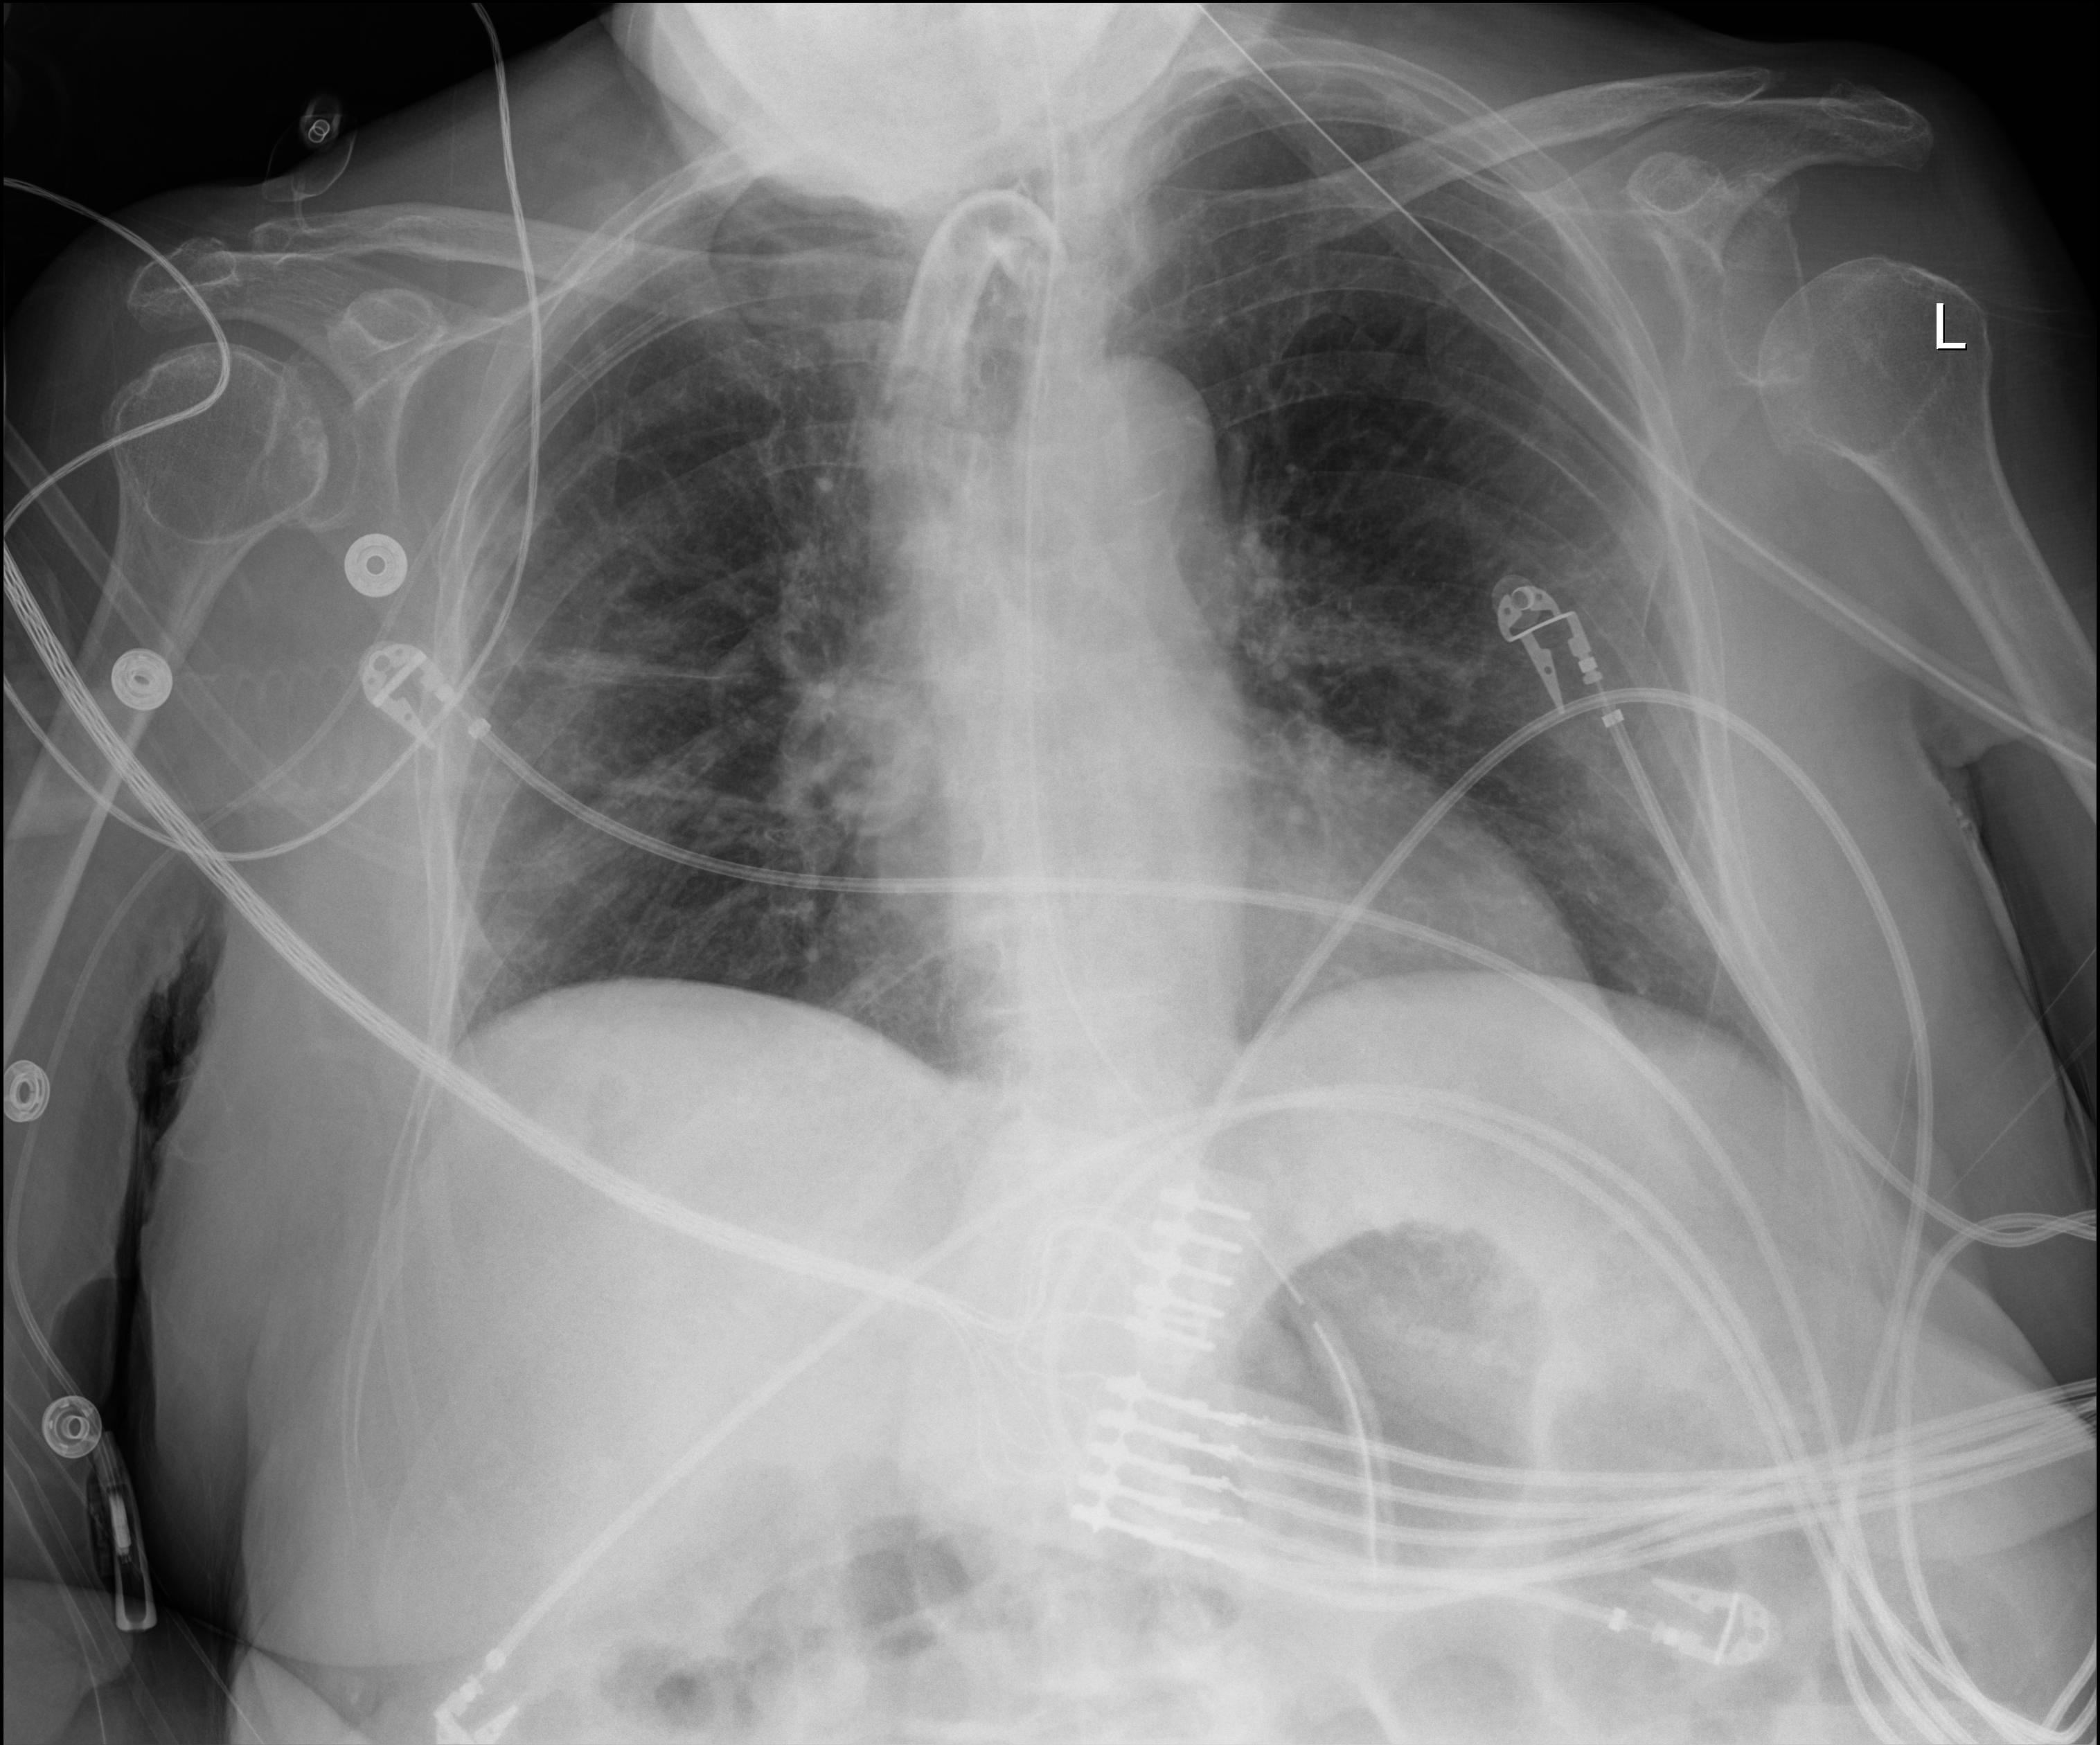
Chest X-ray; anteroposterior (AP) projection. Female patient hospitalised with COVID-19, age 75–90 years.
Admission-level facts for this patient (not findings on this image; timing relative to this image not recorded): admitted to intensive care during this hospital stay: yes; mechanically ventilated during this hospital stay: yes.